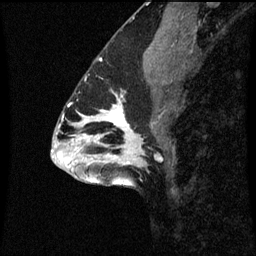
Breast MRI (dynamic contrast-enhanced), one sagittal slice. Position 32 of 60 along the scan axis. Dynamic contrast-enhanced series, image 2 of 3 at this slice position (ordered by acquisition). 1.5 T. TE 4.2 ms, TR 8.9 ms. 2 mm slice thickness. 256 × 256 image matrix, field of view 200 × 200 mm. Patient: female, 43 years. Case-level facts recorded for this patient, not image findings: setting: breast cancer imaged before/during neoadjuvant chemotherapy; receptor status: HR-positive, HER2-negative.
Annotated regions visible in this slice (semi-automatic segmentation, software-assisted and operator-edited):
- analysis volume of interest (the breast-tissue region the enhancement analysis was run in; not a lesion): bounding box (x1, y1, x2, y2) in pixels: (96, 96, 159, 159)
- tumour enhancement mask (voxels above the 70 % enhancement threshold inside the analysis volume of interest): (102, 98, 129, 127)